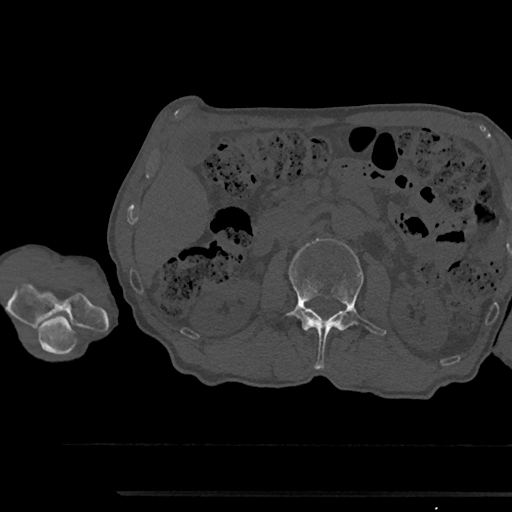
CT including the spine, one axial slice; position 565 of 797 along the scan axis; bone window (W 1800 / L 400 HU); 512 × 512 image matrix, field of view 367 × 367 mm. Male patient, age 79 years. Case-level facts recorded for this patient, not image findings: primary cancer: prostate.
Structures marked on this image (semi-automatically segmented with operator editing):
- L2 vertebra: box from (x=286, y=238) to (x=386, y=369) px